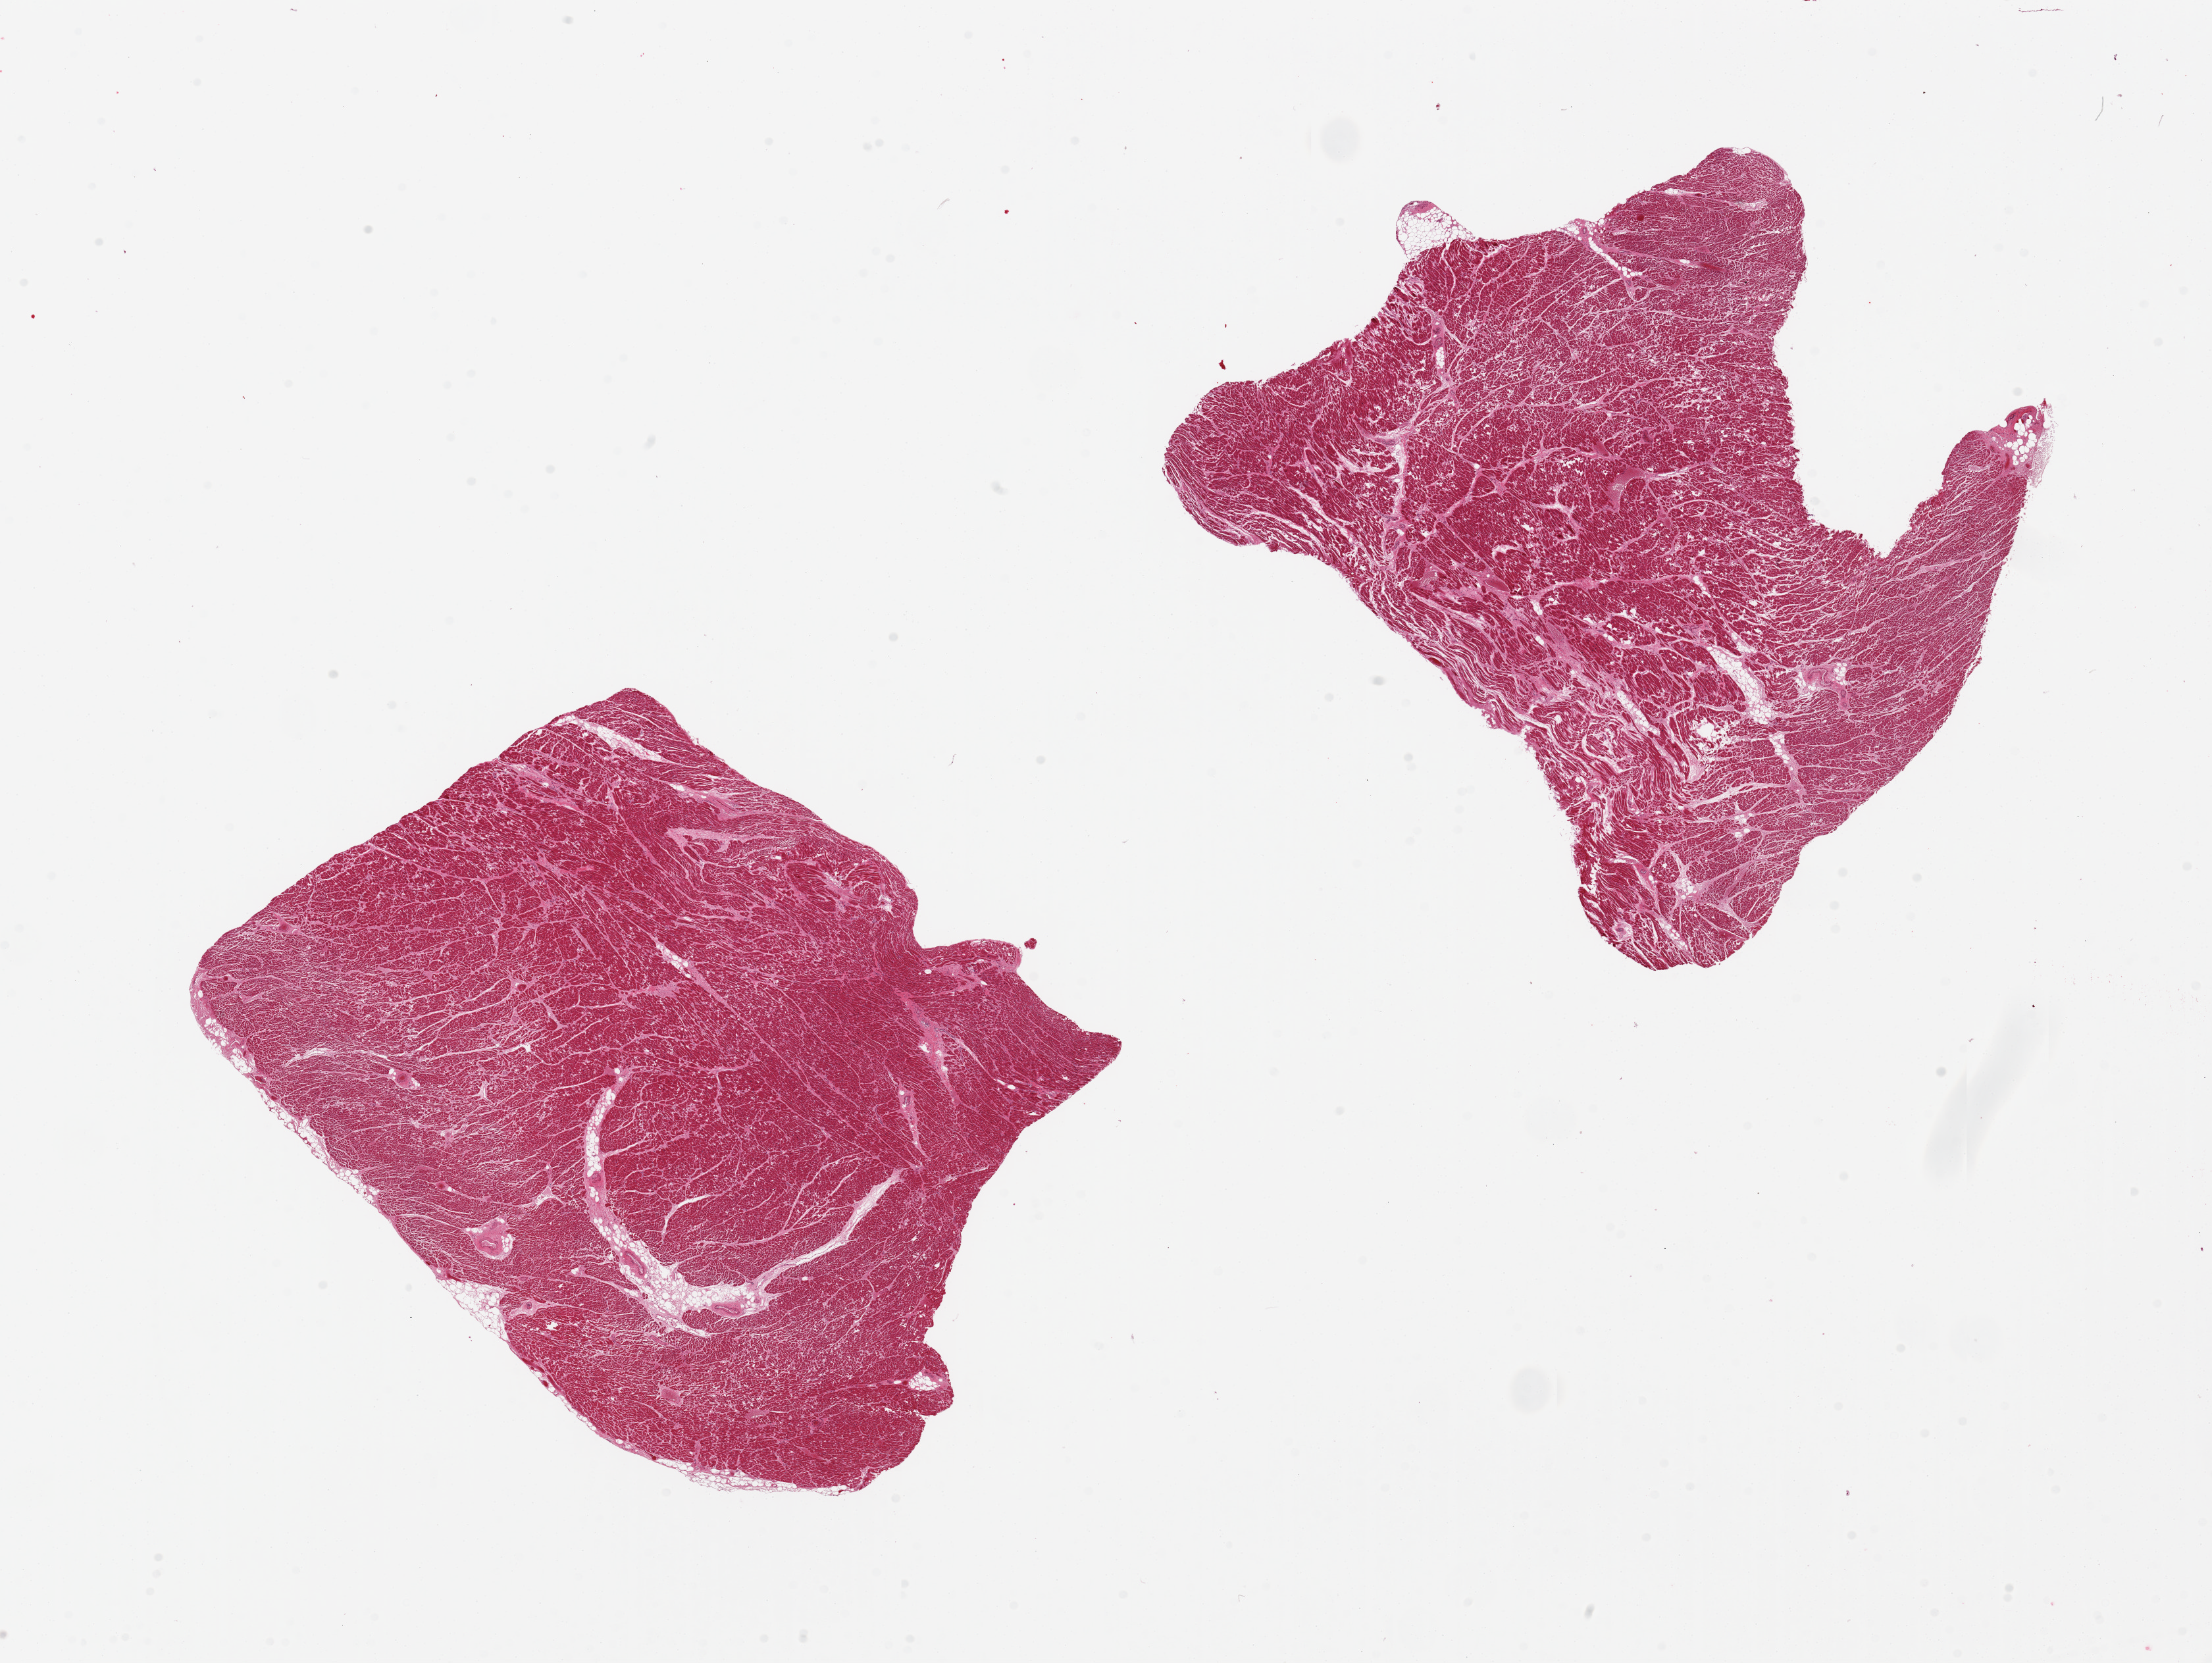
Whole-slide image, haematoxylin and eosin stain — a low-resolution overview of the entire scanned area, about 26.6 x 20.0 mm (slide scanned at 20x); PAXgene-fixed paraffin-embedded (PFPE) section; target tissue: heart; donor tissue sample. Male donor.
Pathologist's review note for this sample: 2 pieces, patchy mild-moderated interstitial fibrosis.